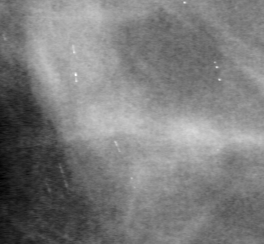
Region of interest cut from a scanned film mammogram (one marked finding), left breast, CC view.
Mass, shape lobulated, margins circumscribed; BI-RADS assessment category 4; subtlety rating 3 on a 1 (subtle) to 5 (obvious) scale; pathology result (as recorded, not read from the image): benign.